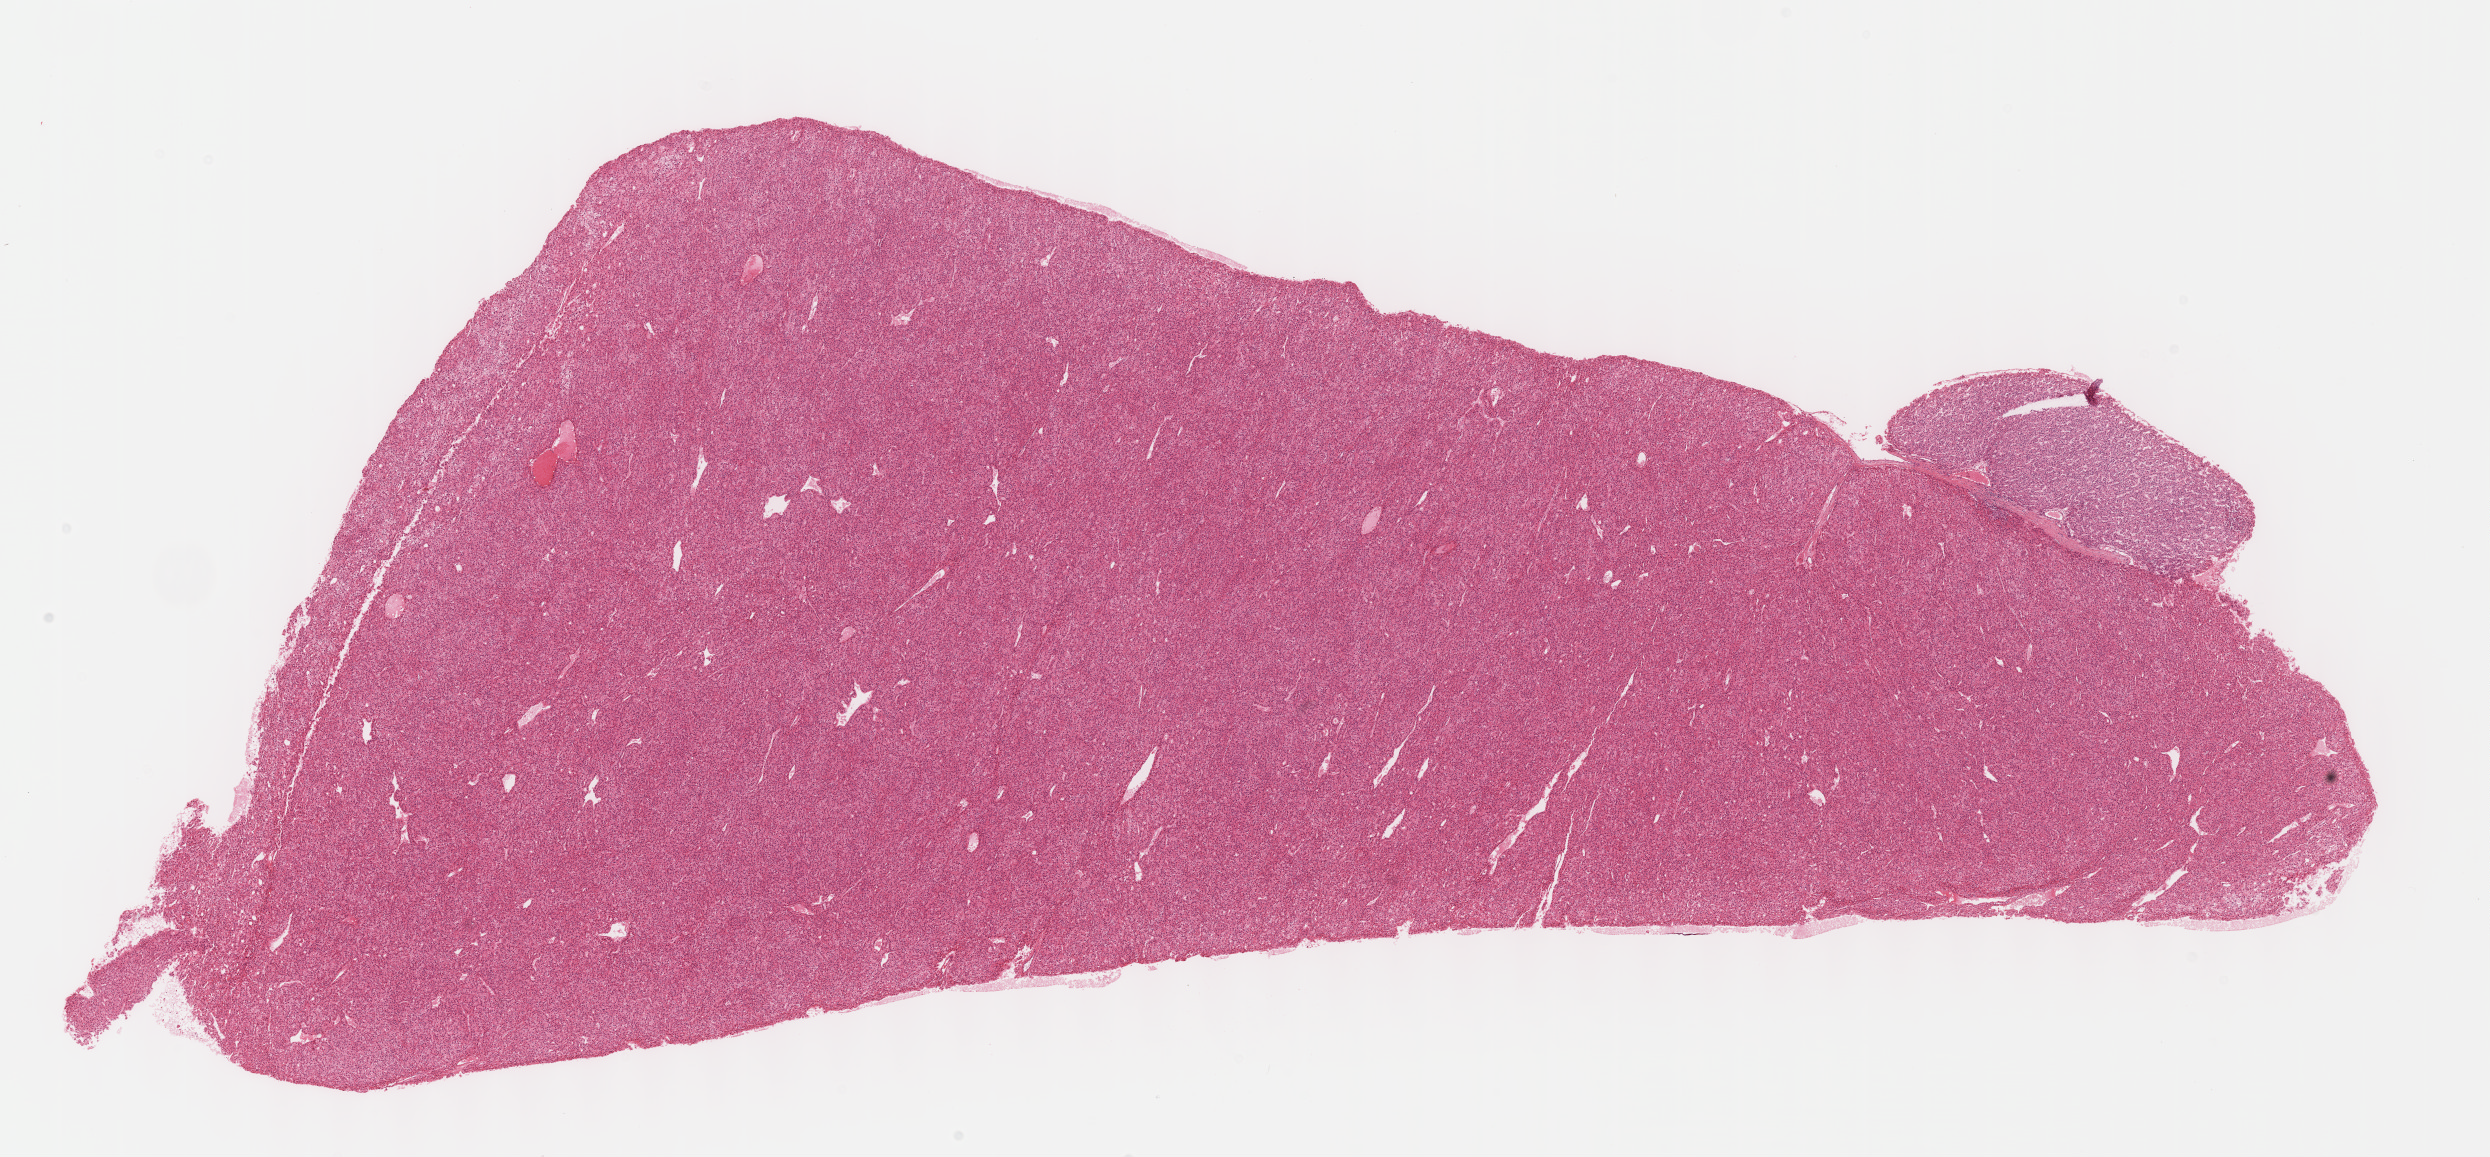
H&E-stained whole-slide image, whole scanned area (about 20.1 x 9.3 mm) shown as a low-resolution overview, FFPE section, sample: primary tumour, liver. Patient: male, age at initial diagnosis 70 years. Histologic grade: G3 (poorly differentiated).
- pathologic diagnosis: Hepatocellular carcinoma, NOS
- AJCC pathologic stage: IIIA (7th edition)